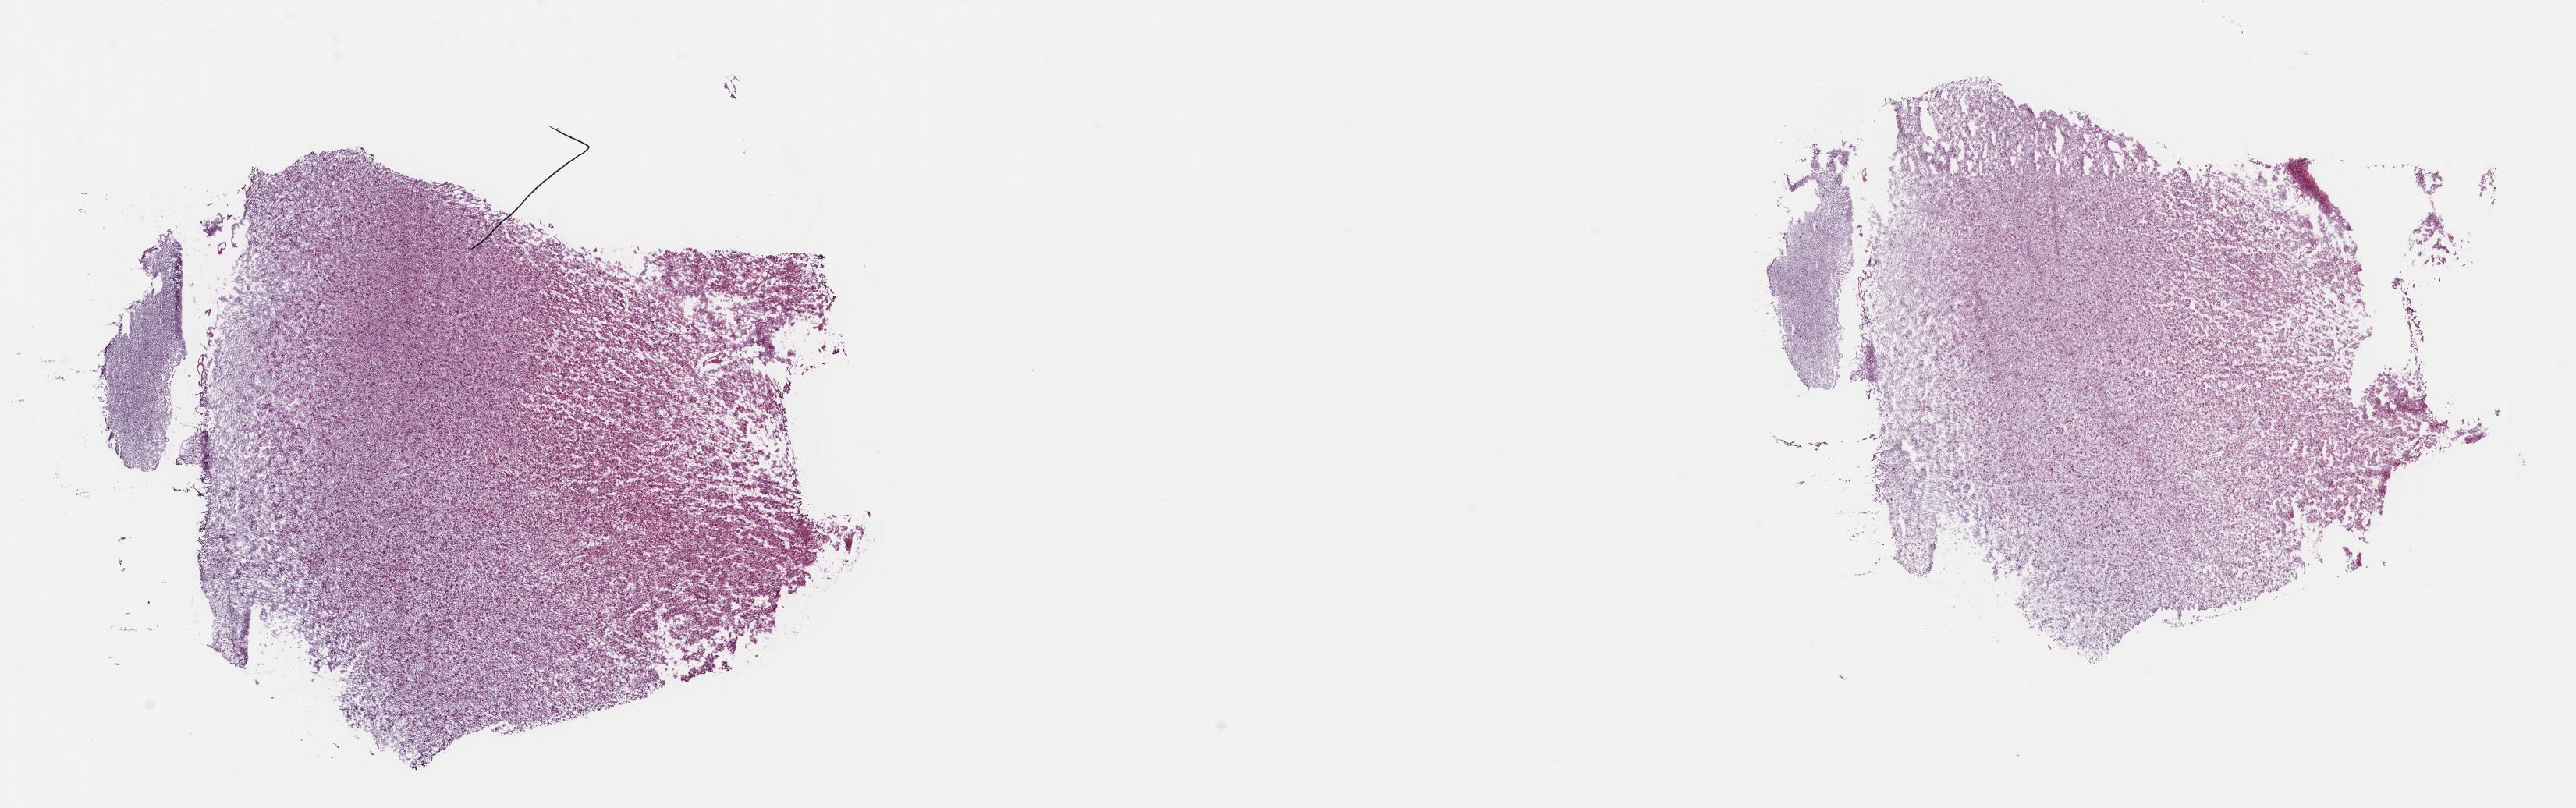
Whole-slide histology image, Hematoxylin and eosin (H&E) stained — shown as a low-resolution overview of the whole scanned area (about 26.0 x 8.2 mm, acquisition: 40x scan); frozen section from the top of the tissue portion; brain, primary tumour sample. Male patient; age at initial diagnosis 59 years. Histologic grade: G2 (moderately differentiated). Pathologist review of this section (percent, as recorded): tumour cells 75%, tumour nuclei 85%, normal cells 5%, stromal cells 20%, necrosis 0%. Infiltration values recorded for this section: lymphocyte infiltration 0%, monocyte infiltration 0%, neutrophil infiltration 0%.
• diagnosis: Mixed glioma (cerebrum)